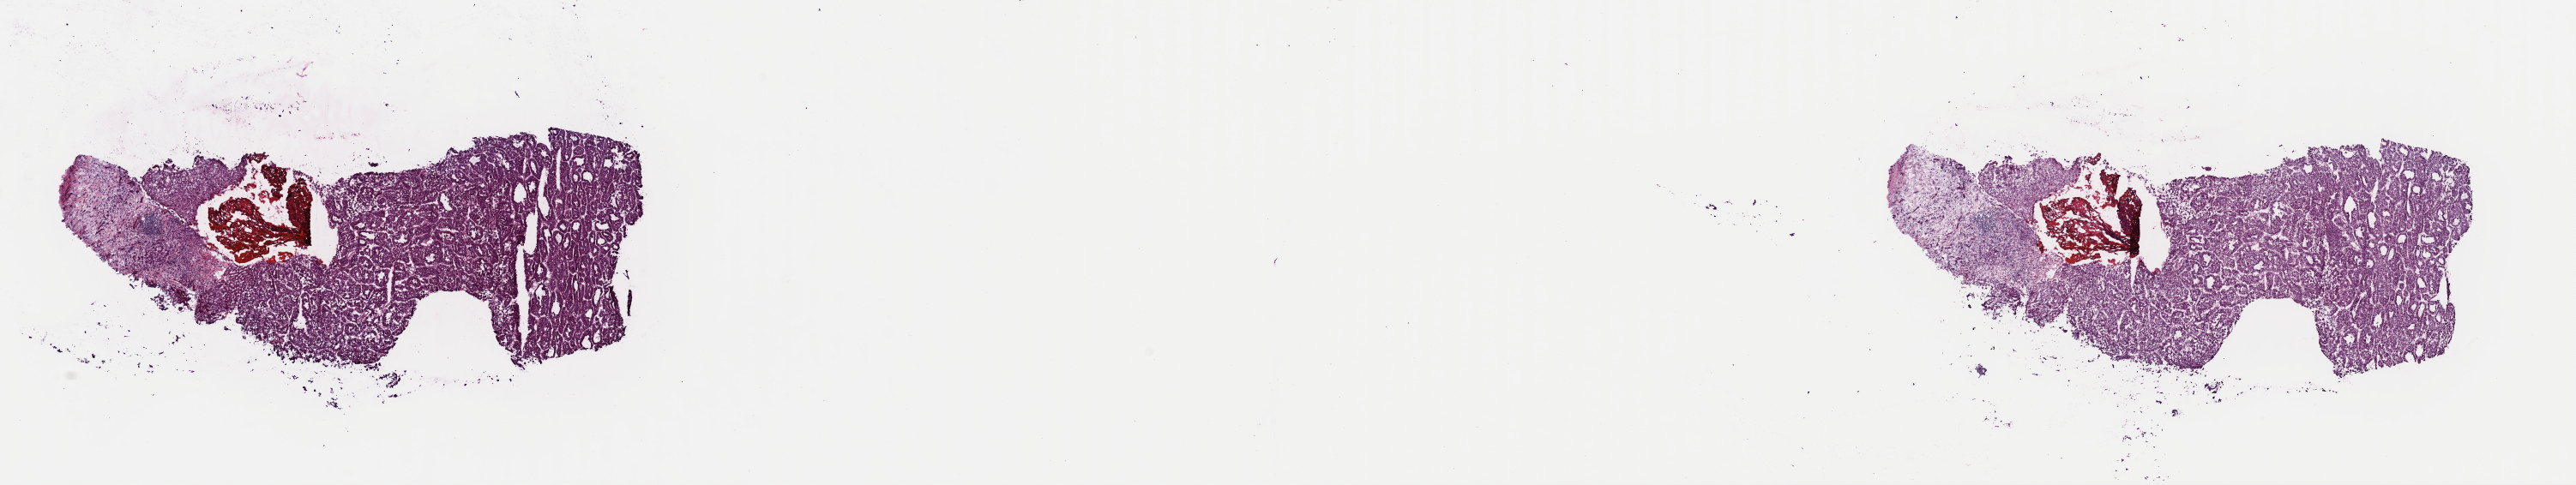
Whole-slide histology image, Hematoxylin and eosin (H&E) stained — low-resolution overview of the scanned area, about 23.7 x 4.5 mm; frozen section; primary tumour sample from the liver. Male patient; age at initial diagnosis 61 years. Histologic grade: G2 (moderately differentiated). Composition of this section per pathologist review: tumour cells 73%, tumour nuclei 88%, normal cells 0%, stromal cells 20%, necrosis 7%. Infiltration values recorded for this section: lymphocyte infiltration 7%, monocyte infiltration 2%, neutrophil infiltration 1%.
AJCC pathologic stage: IIIC (7th edition). TNM: T4 N0 M0. Diagnosis: Hepatocellular carcinoma, NOS.